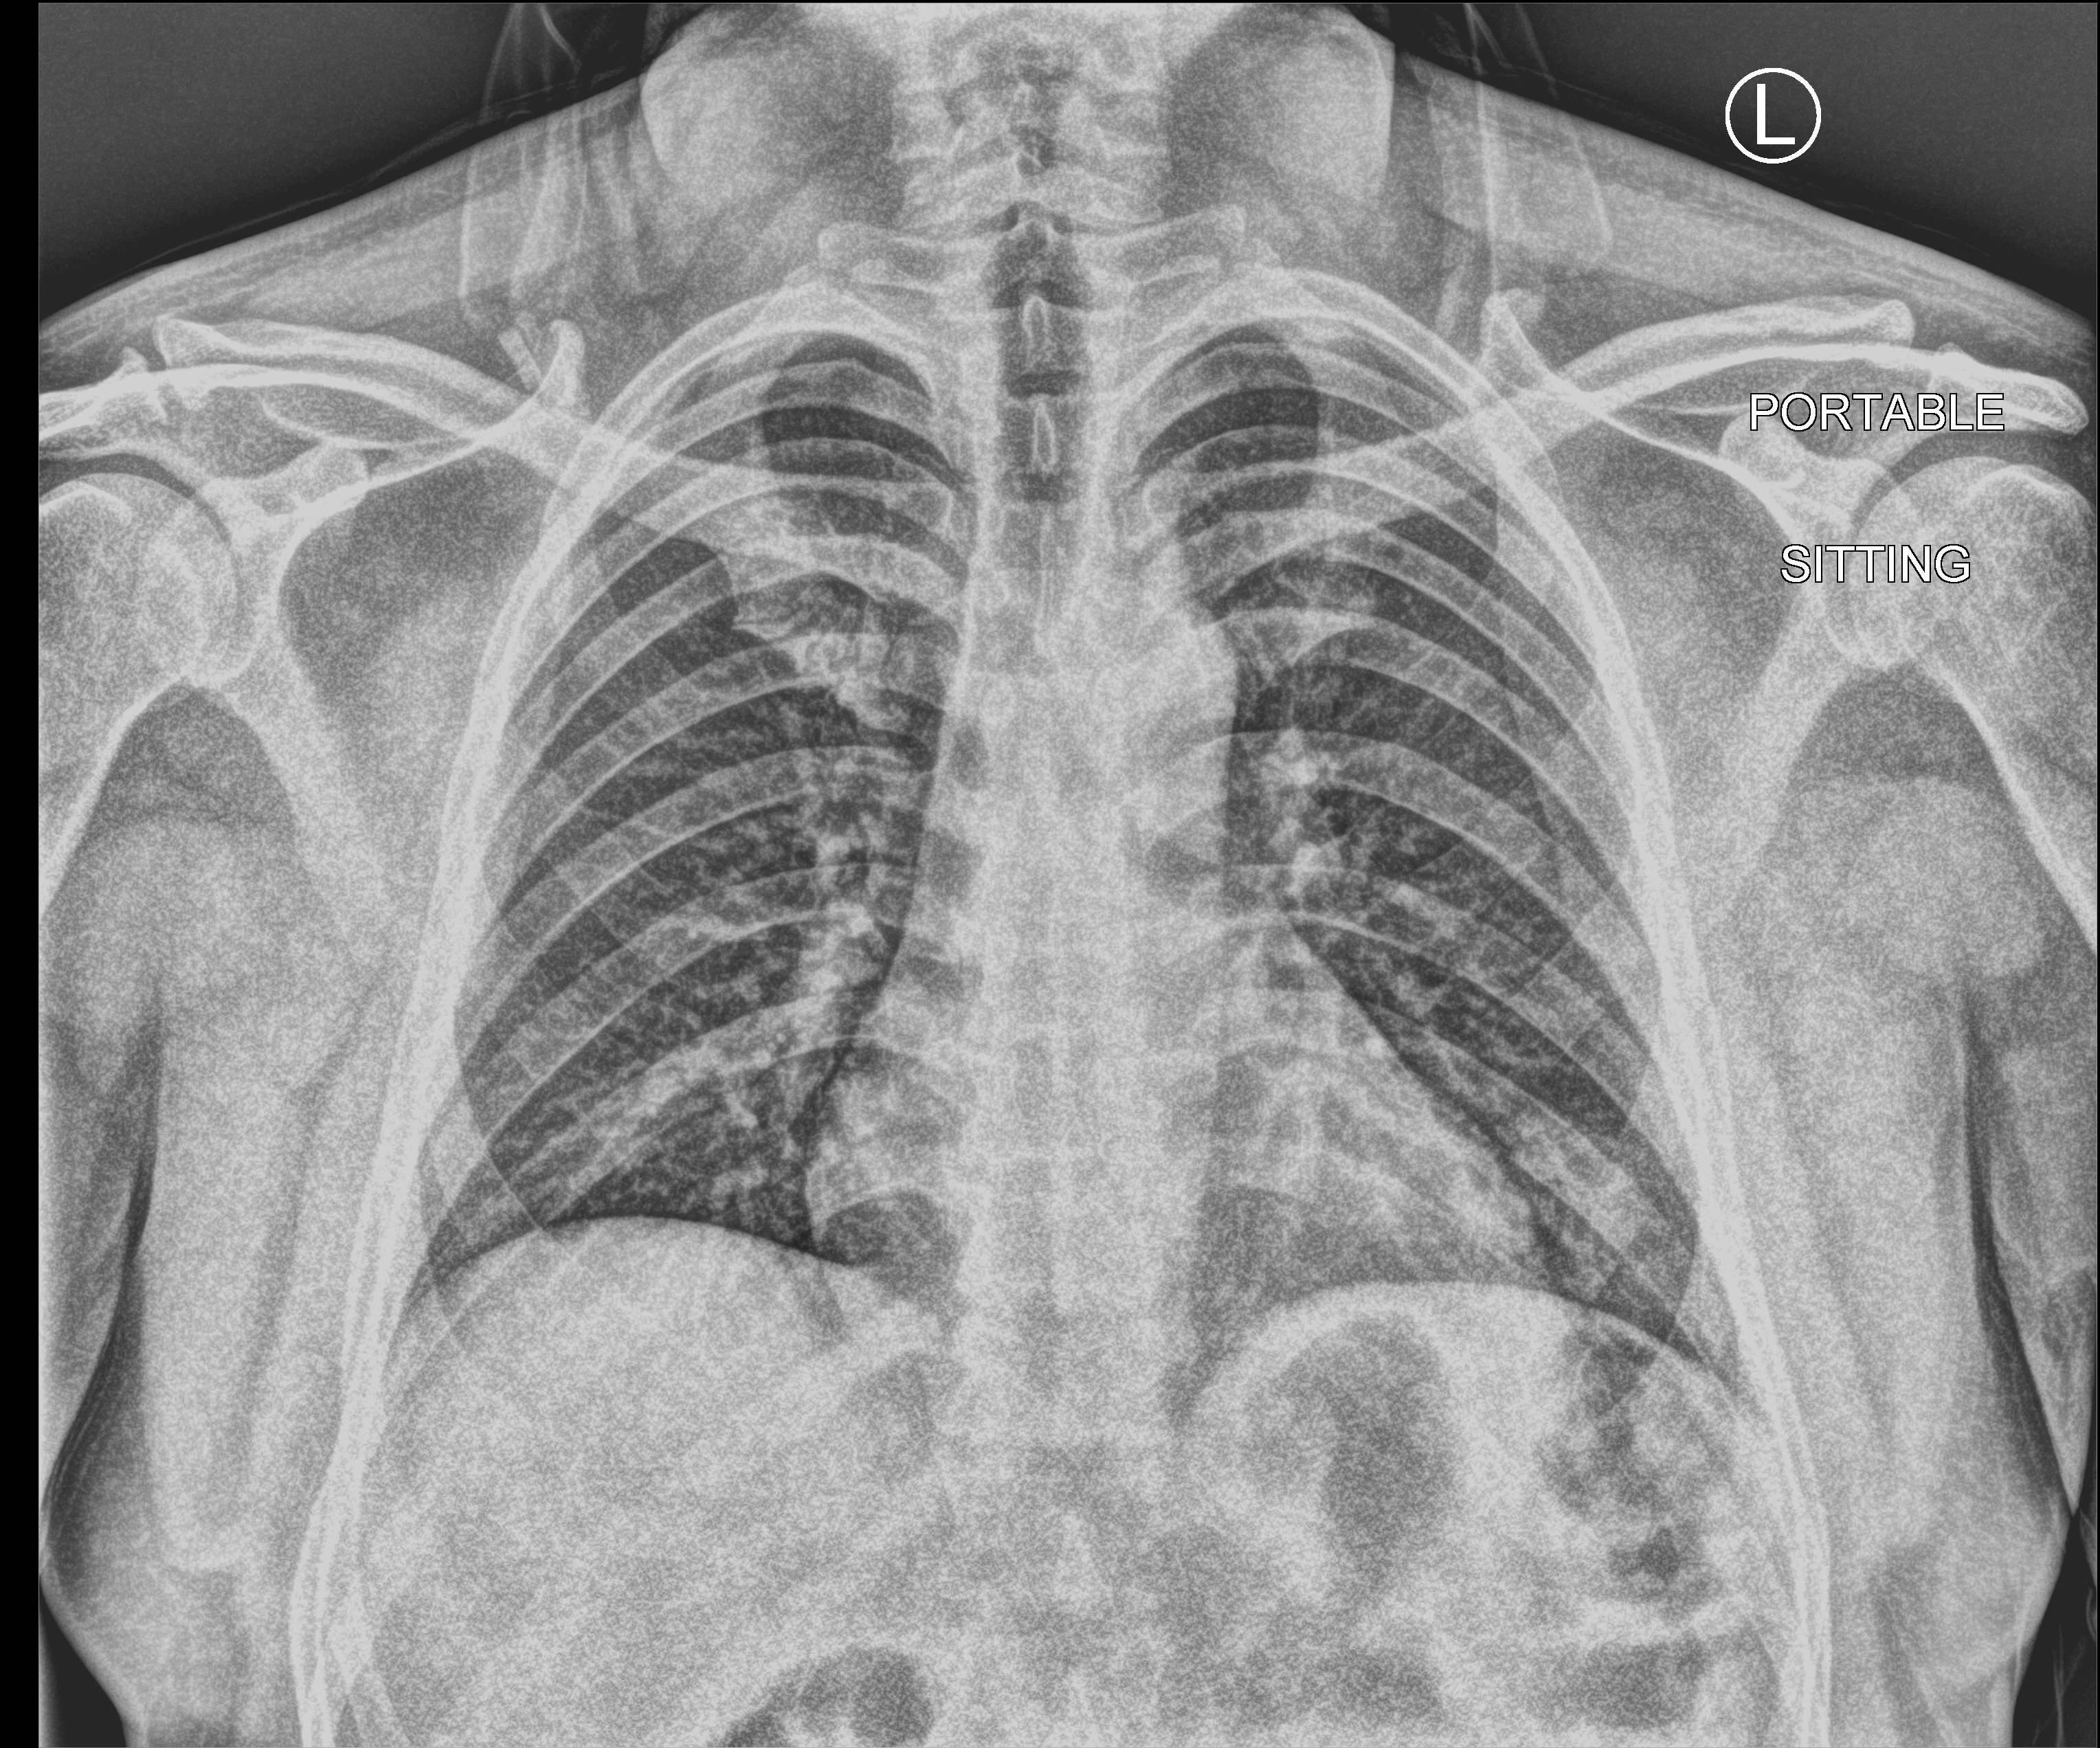
Chest X-ray (portable), anteroposterior (AP) projection. Male patient hospitalised with COVID-19, age 18–59 years.
Hospital-stay facts (about this admission, not read from this image; timing relative to this image not recorded):
- length of hospital stay: 1 day
- mechanically ventilated during this hospital stay: no
- admitted to intensive care during this hospital stay: no